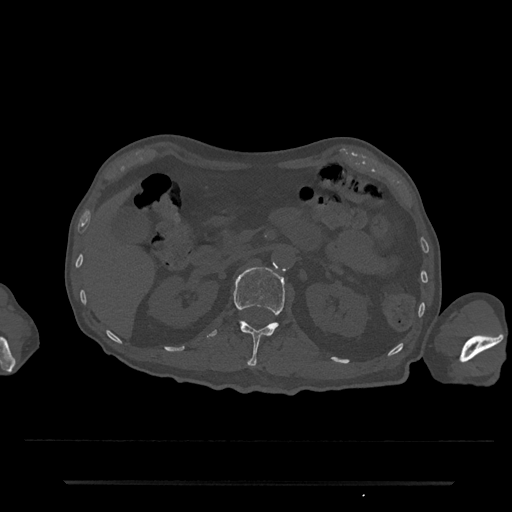
CT including the spine, one axial slice; position 124 of 797 along the scan axis; bone window (W 1800 / L 400 HU); 512 × 512 image matrix, field of view 427 × 427 mm. Male patient, age 74 years. From the clinical record (not read from this slice): primary cancer: prostate.
Structures marked on this image (semi-automatically segmented with operator editing):
- L1 vertebra: bounding box (x1, y1, x2, y2) in pixels: (206, 267, 285, 366)